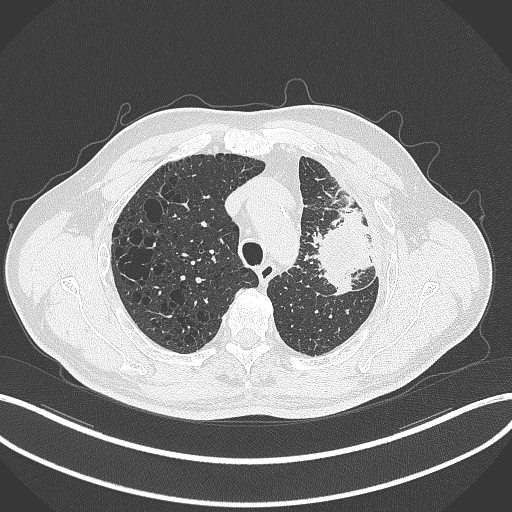
Chest CT, one axial slice. Position 247 of 297 along the scan axis. 120 kVp. Lung window (W 1500 / L -600 HU). 1 mm slice thickness. 512 × 512 image matrix. Male patient, age 68 years. From the clinical record (not read from this slice): clinical TNM (as recorded): T3 N3 M1.
Annotated regions visible in this slice (bounding box drawn by a radiologist):
- lung tumour (recorded histology: adenocarcinoma): bounding box <308,202,371,300> (left, top, right, bottom; pixels)